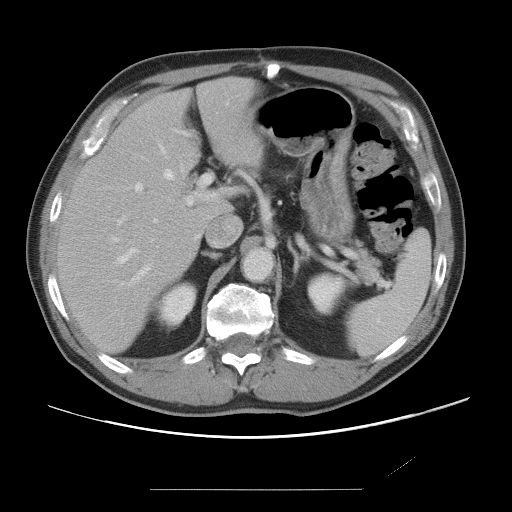
Contrast-enhanced abdominal CT, one axial slice. Slice 46 of 87 in the series (ordered by position). Soft-tissue window (W 400 / L 40 HU). 512 × 512 image matrix. Male patient, age 74 years. From the clinical record (not read from this slice): diagnosis: colorectal cancer liver metastases, imaged before liver resection; multiple liver metastases: yes; largest metastasis: 1.1 cm; chemotherapy before resection: yes.
Structures marked on this image (manually delineated by an expert):
- hepatic veins: bounding box [x1, y1, x2, y2] px = [113, 146, 183, 263]
- liver: [59, 77, 264, 351]
- planned liver remnant (the part of the liver to remain after resection): [59, 78, 264, 351]
- portal vein (with intrahepatic branches): [117, 174, 218, 281]